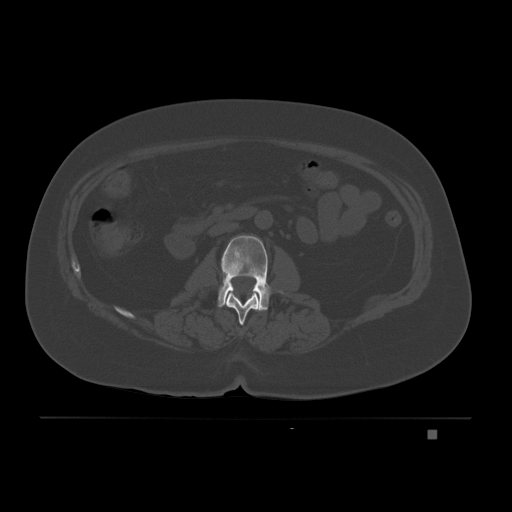
CT including the spine, one axial slice. Slice 65 of 221 in the series (ordered by position). Bone window (W 1800 / L 400 HU). 3 mm slice thickness. 512 × 512 image matrix. Female patient, age 63 years. Case-level facts recorded for this patient, not image findings: primary cancer: breast.
Outlined on this slice (semi-automatic segmentation, software-assisted and operator-edited):
- L1 vertebra: bounding box [x1, y1, x2, y2] px = [223, 291, 262, 325]
- L2 vertebra: [218, 235, 283, 310]